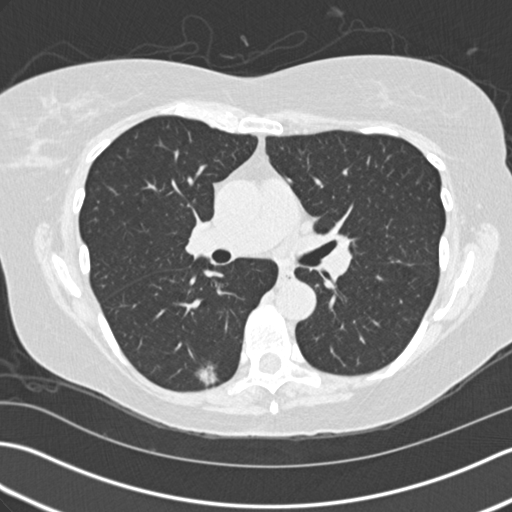
Low-dose screening chest CT, one axial slice; slice 88 of 159 in the series (ordered by position); 120 kVp; lung window (W 1500 / L -600 HU); 2 mm slice thickness; 512 × 512 image matrix, field of view 350 × 350 mm.
Outlined on this slice (outlined manually by an expert reader):
- lesion 1 (tumor, lower lobe of right lung): bounding box [x1, y1, x2, y2] px = [194, 362, 218, 386]